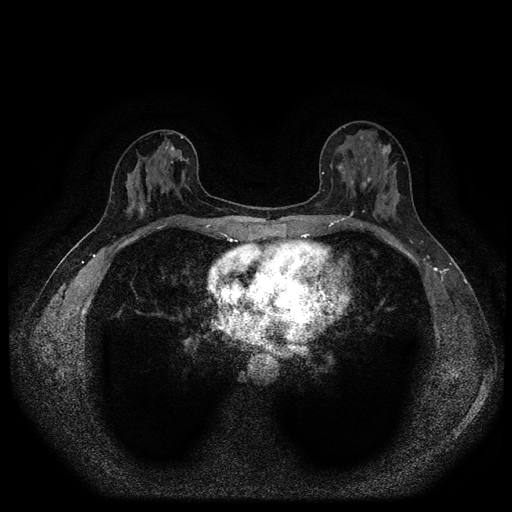
Breast MRI (dynamic contrast-enhanced, multi-phase), one axial slice. Slice 40 of 116 in the series (ordered by position). Dynamic contrast-enhanced series, time point 2 of 5 at this slice position (early post-contrast). 1.5 T. TE 2.7 ms, TR 5.4 ms. 2 mm slice thickness. 512 × 512 image matrix. Patient: female, 42 years.
Outlined on this slice (semi-automatic segmentation, software-assisted and operator-edited):
- breast lesion (labelled benign in the annotation): box from (x=377, y=142) to (x=391, y=159) px